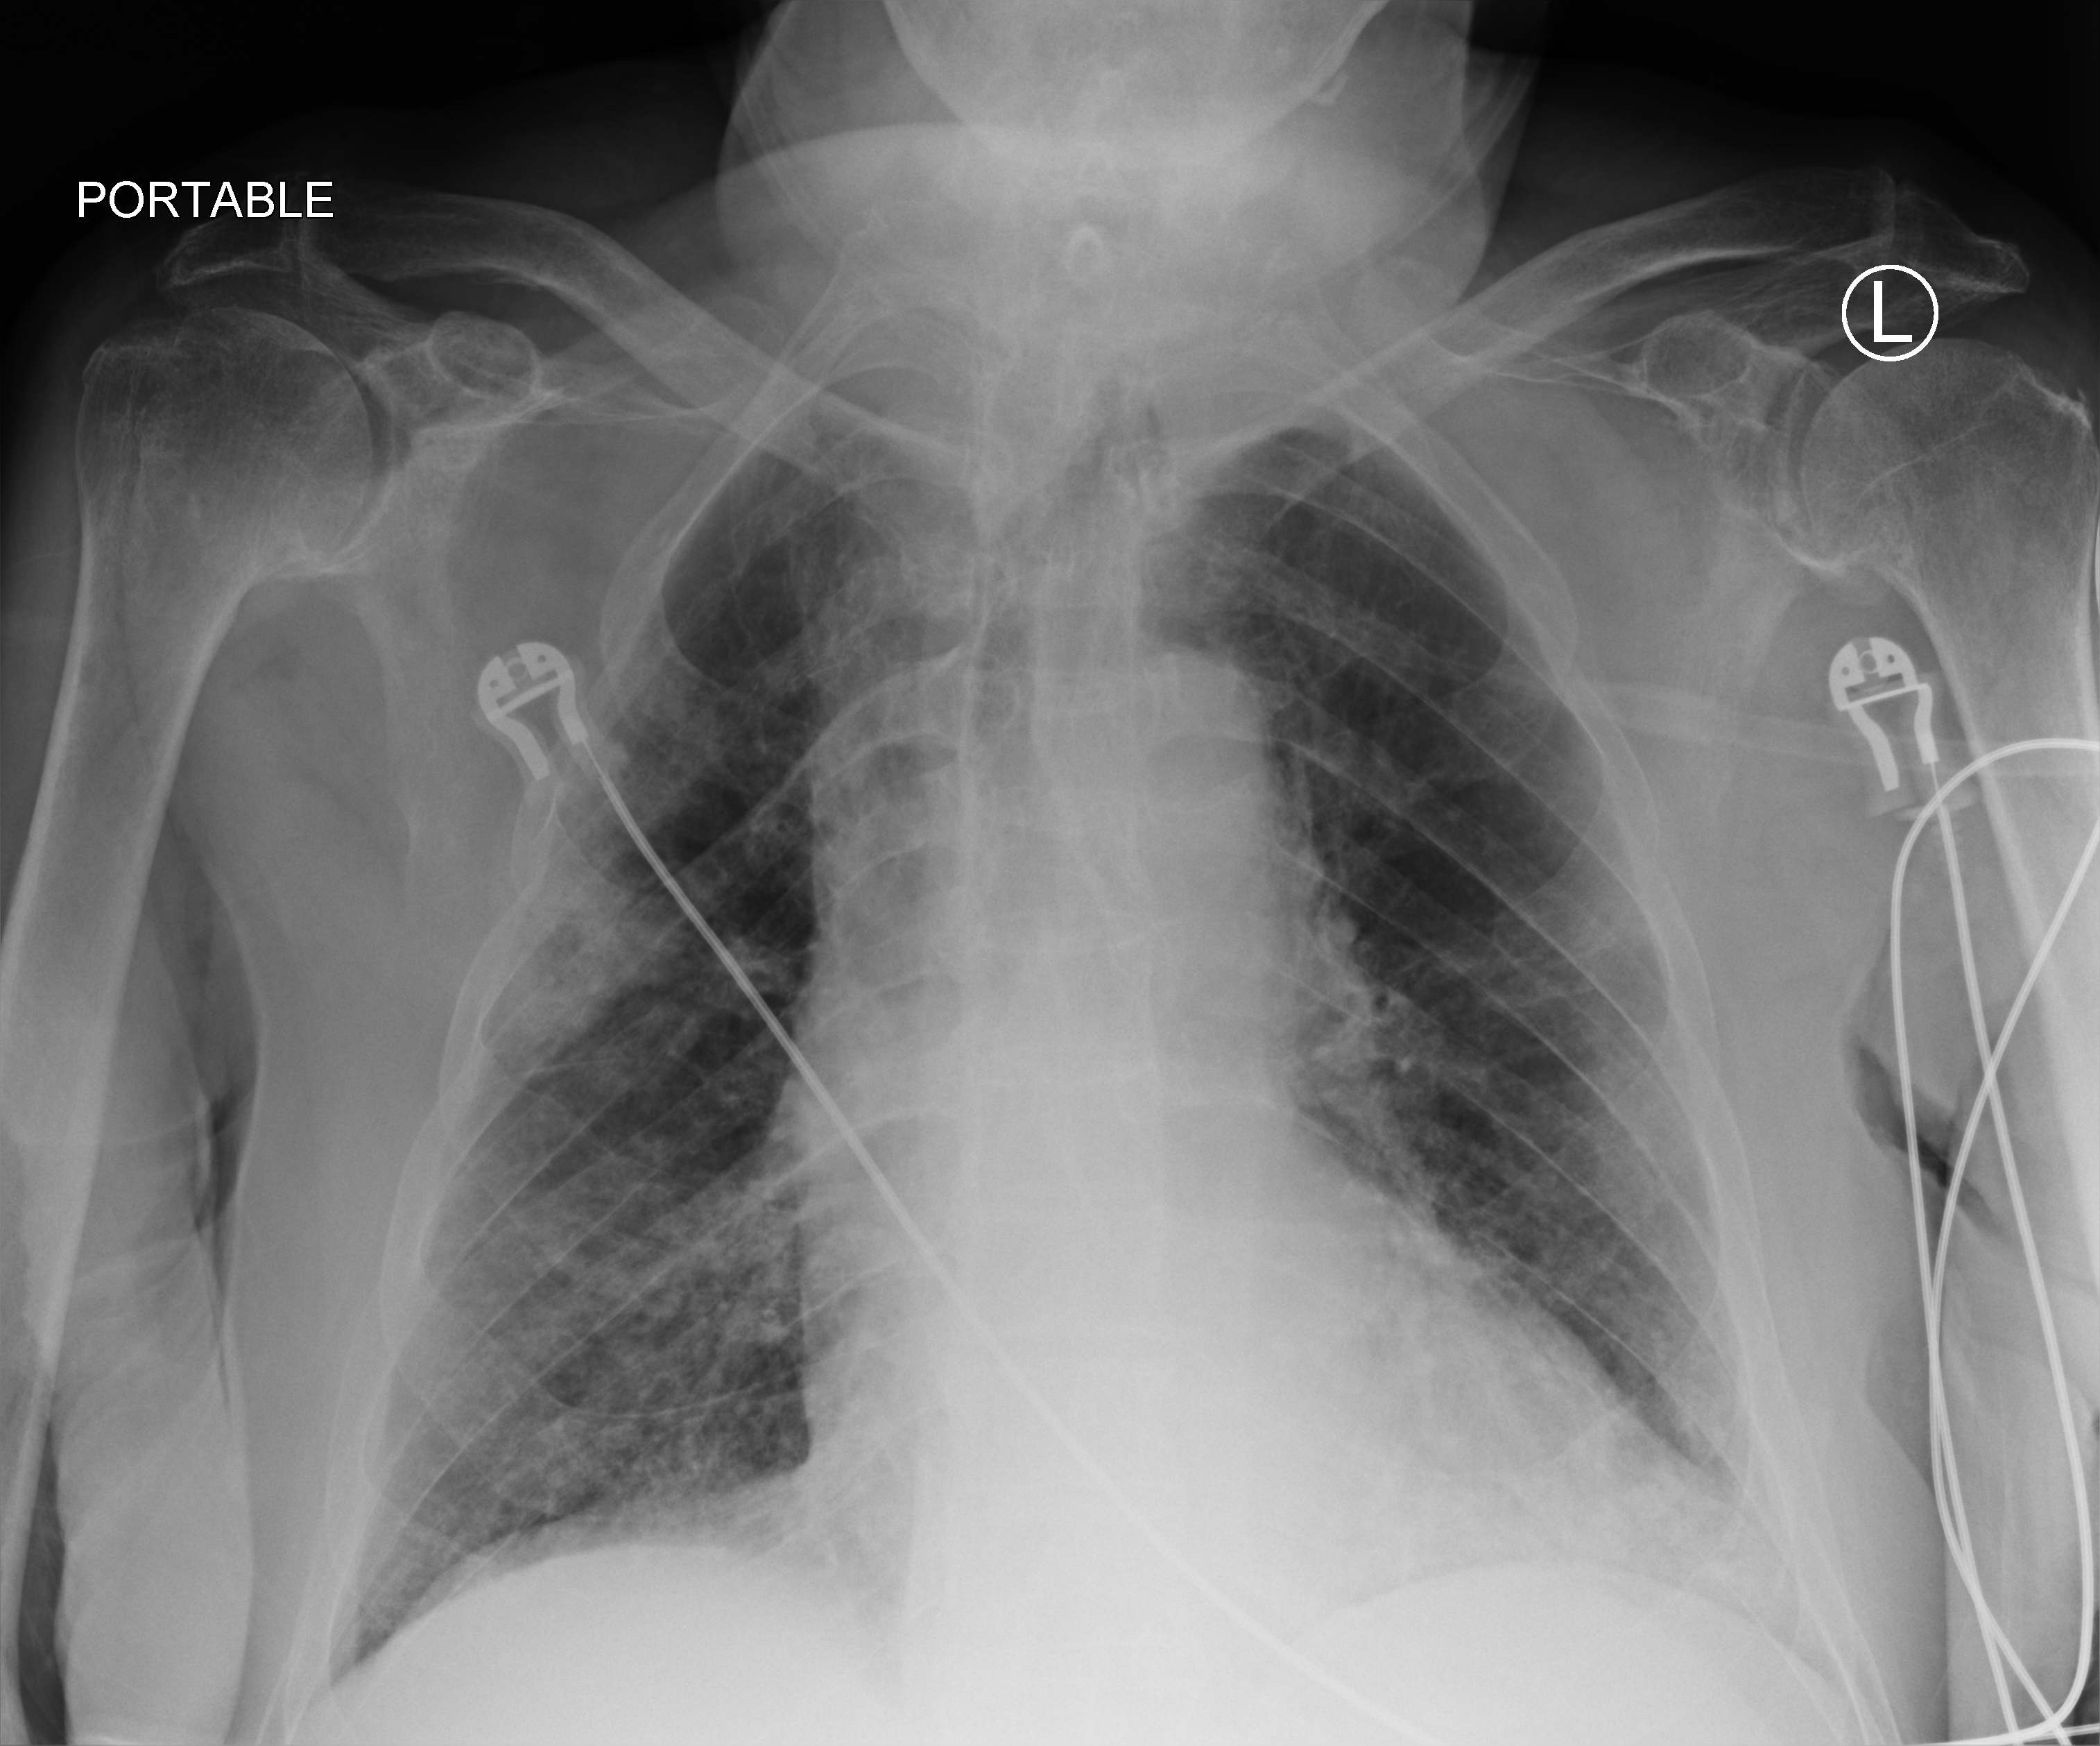
Chest X-ray (portable); anteroposterior (AP) projection. Patient hospitalised with COVID-19; male, aged 75–90 years.
Admission-level facts for this patient (not findings on this image; timing relative to this image not recorded): mechanically ventilated during this hospital stay: no; admitted to intensive care during this hospital stay: no.